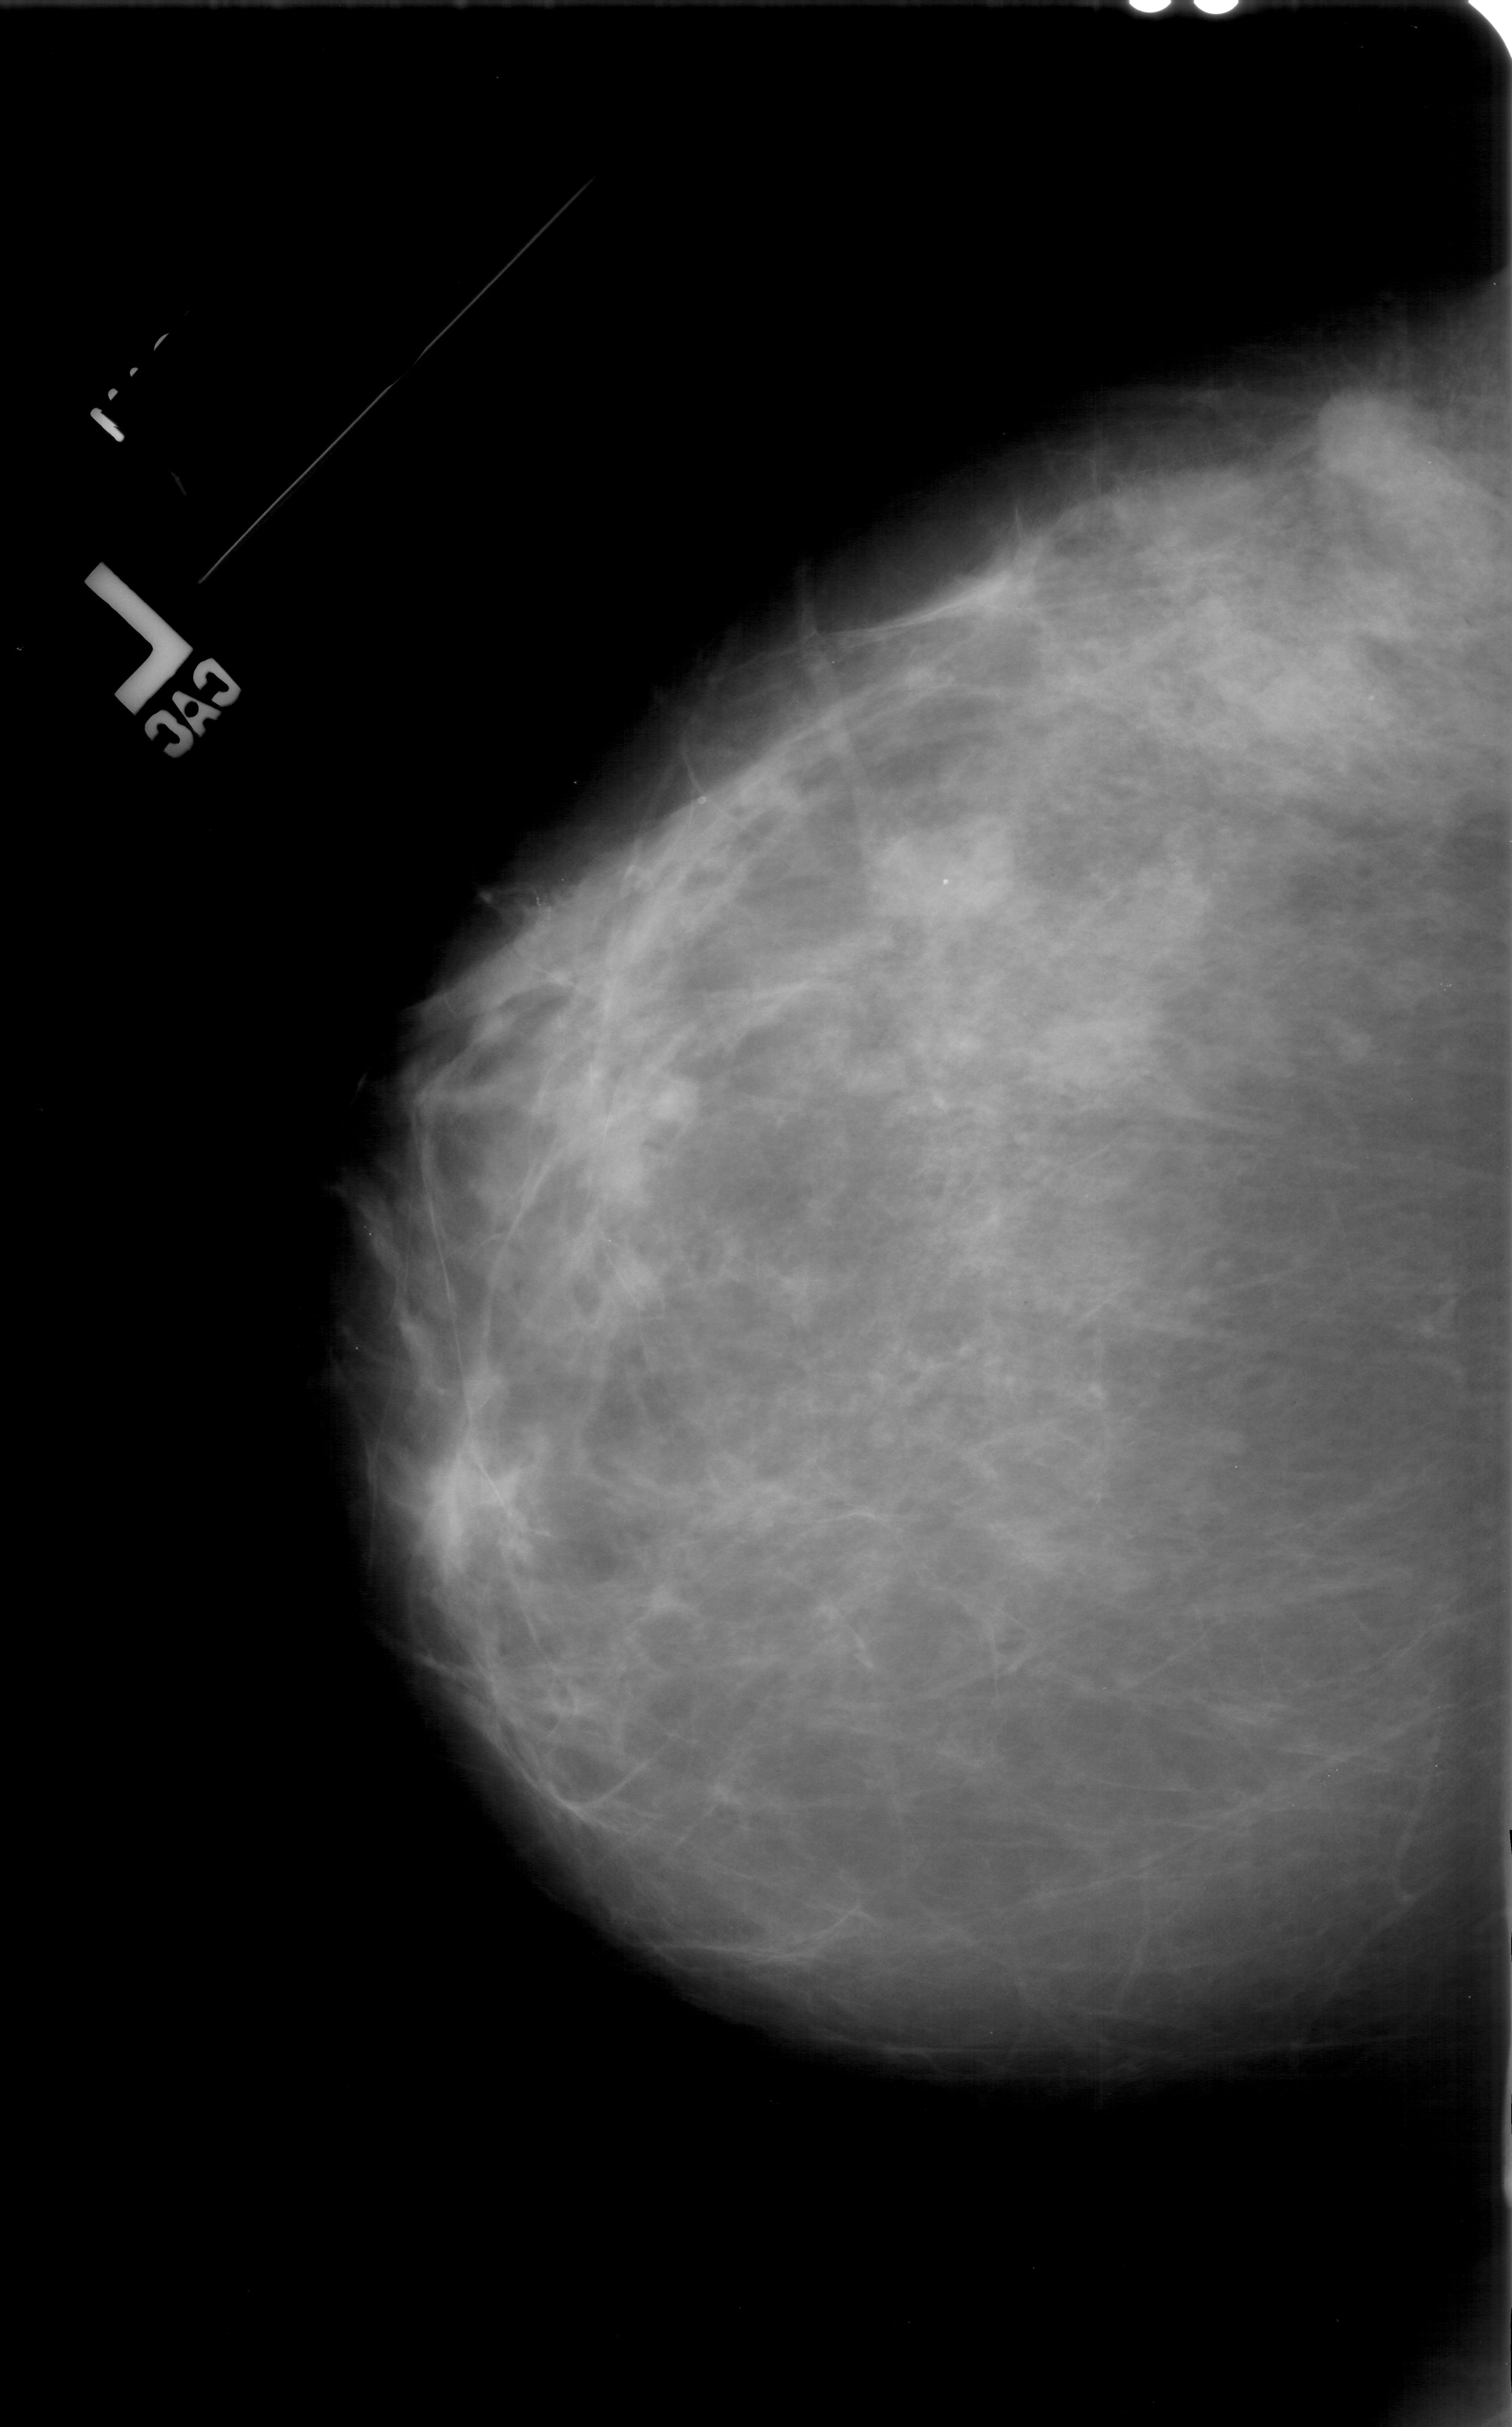
Scanned film-screen mammogram; left breast; CC view; BI-RADS breast density category 3 (scale 1–4); 1512 × 2427 image matrix.
Marked abnormalities (boxes around the expert regions of interest):
- mass, shape lobulated, margins ill defined; BI-RADS assessment category 4; pathology (as recorded): malignant: box from (x=1327, y=382) to (x=1418, y=482) px